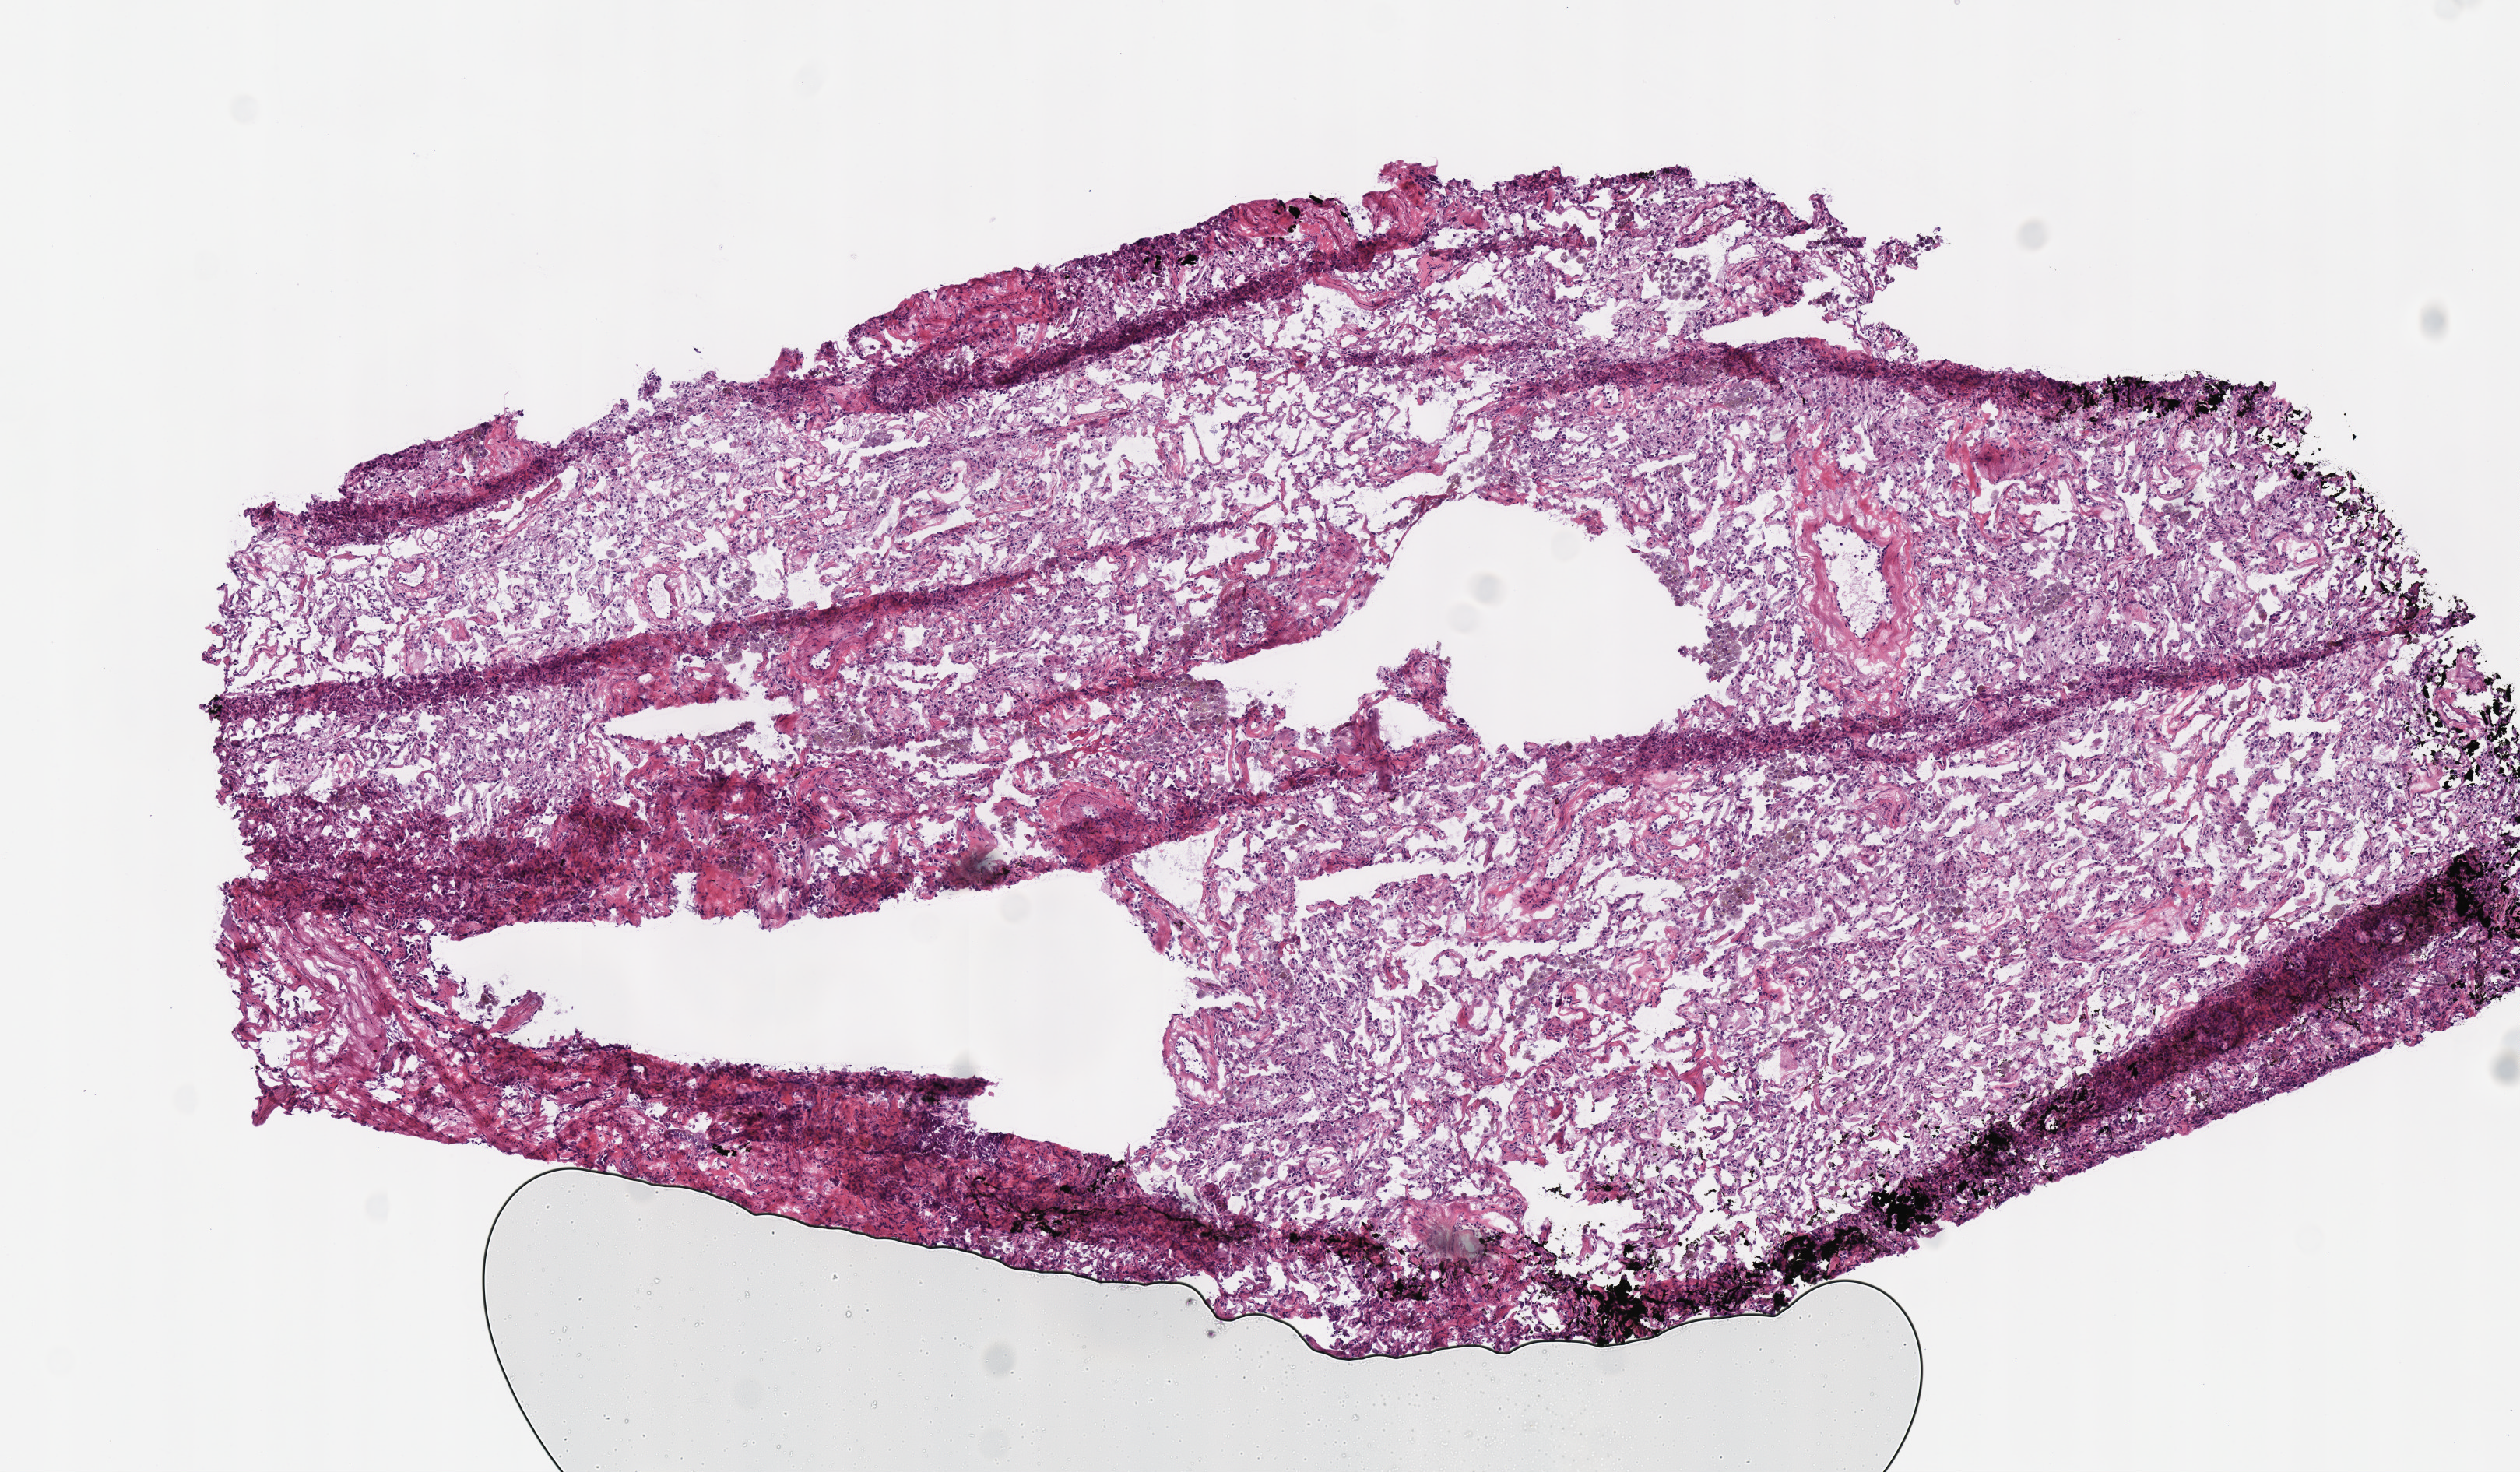
Whole-slide histology image, H&E — a low-resolution overview of the entire scanned area, about 6.4 x 3.7 mm (slide scanned at 40x). Frozen section from the top of the tissue portion. Sample: solid tissue normal (non-tumour tissue), lung. Female, age 66 years at initial diagnosis.
* this section: solid tissue normal sample (biorepository sample class)
* patient diagnosis: Squamous cell carcinoma, NOS (upper lobe, lung)